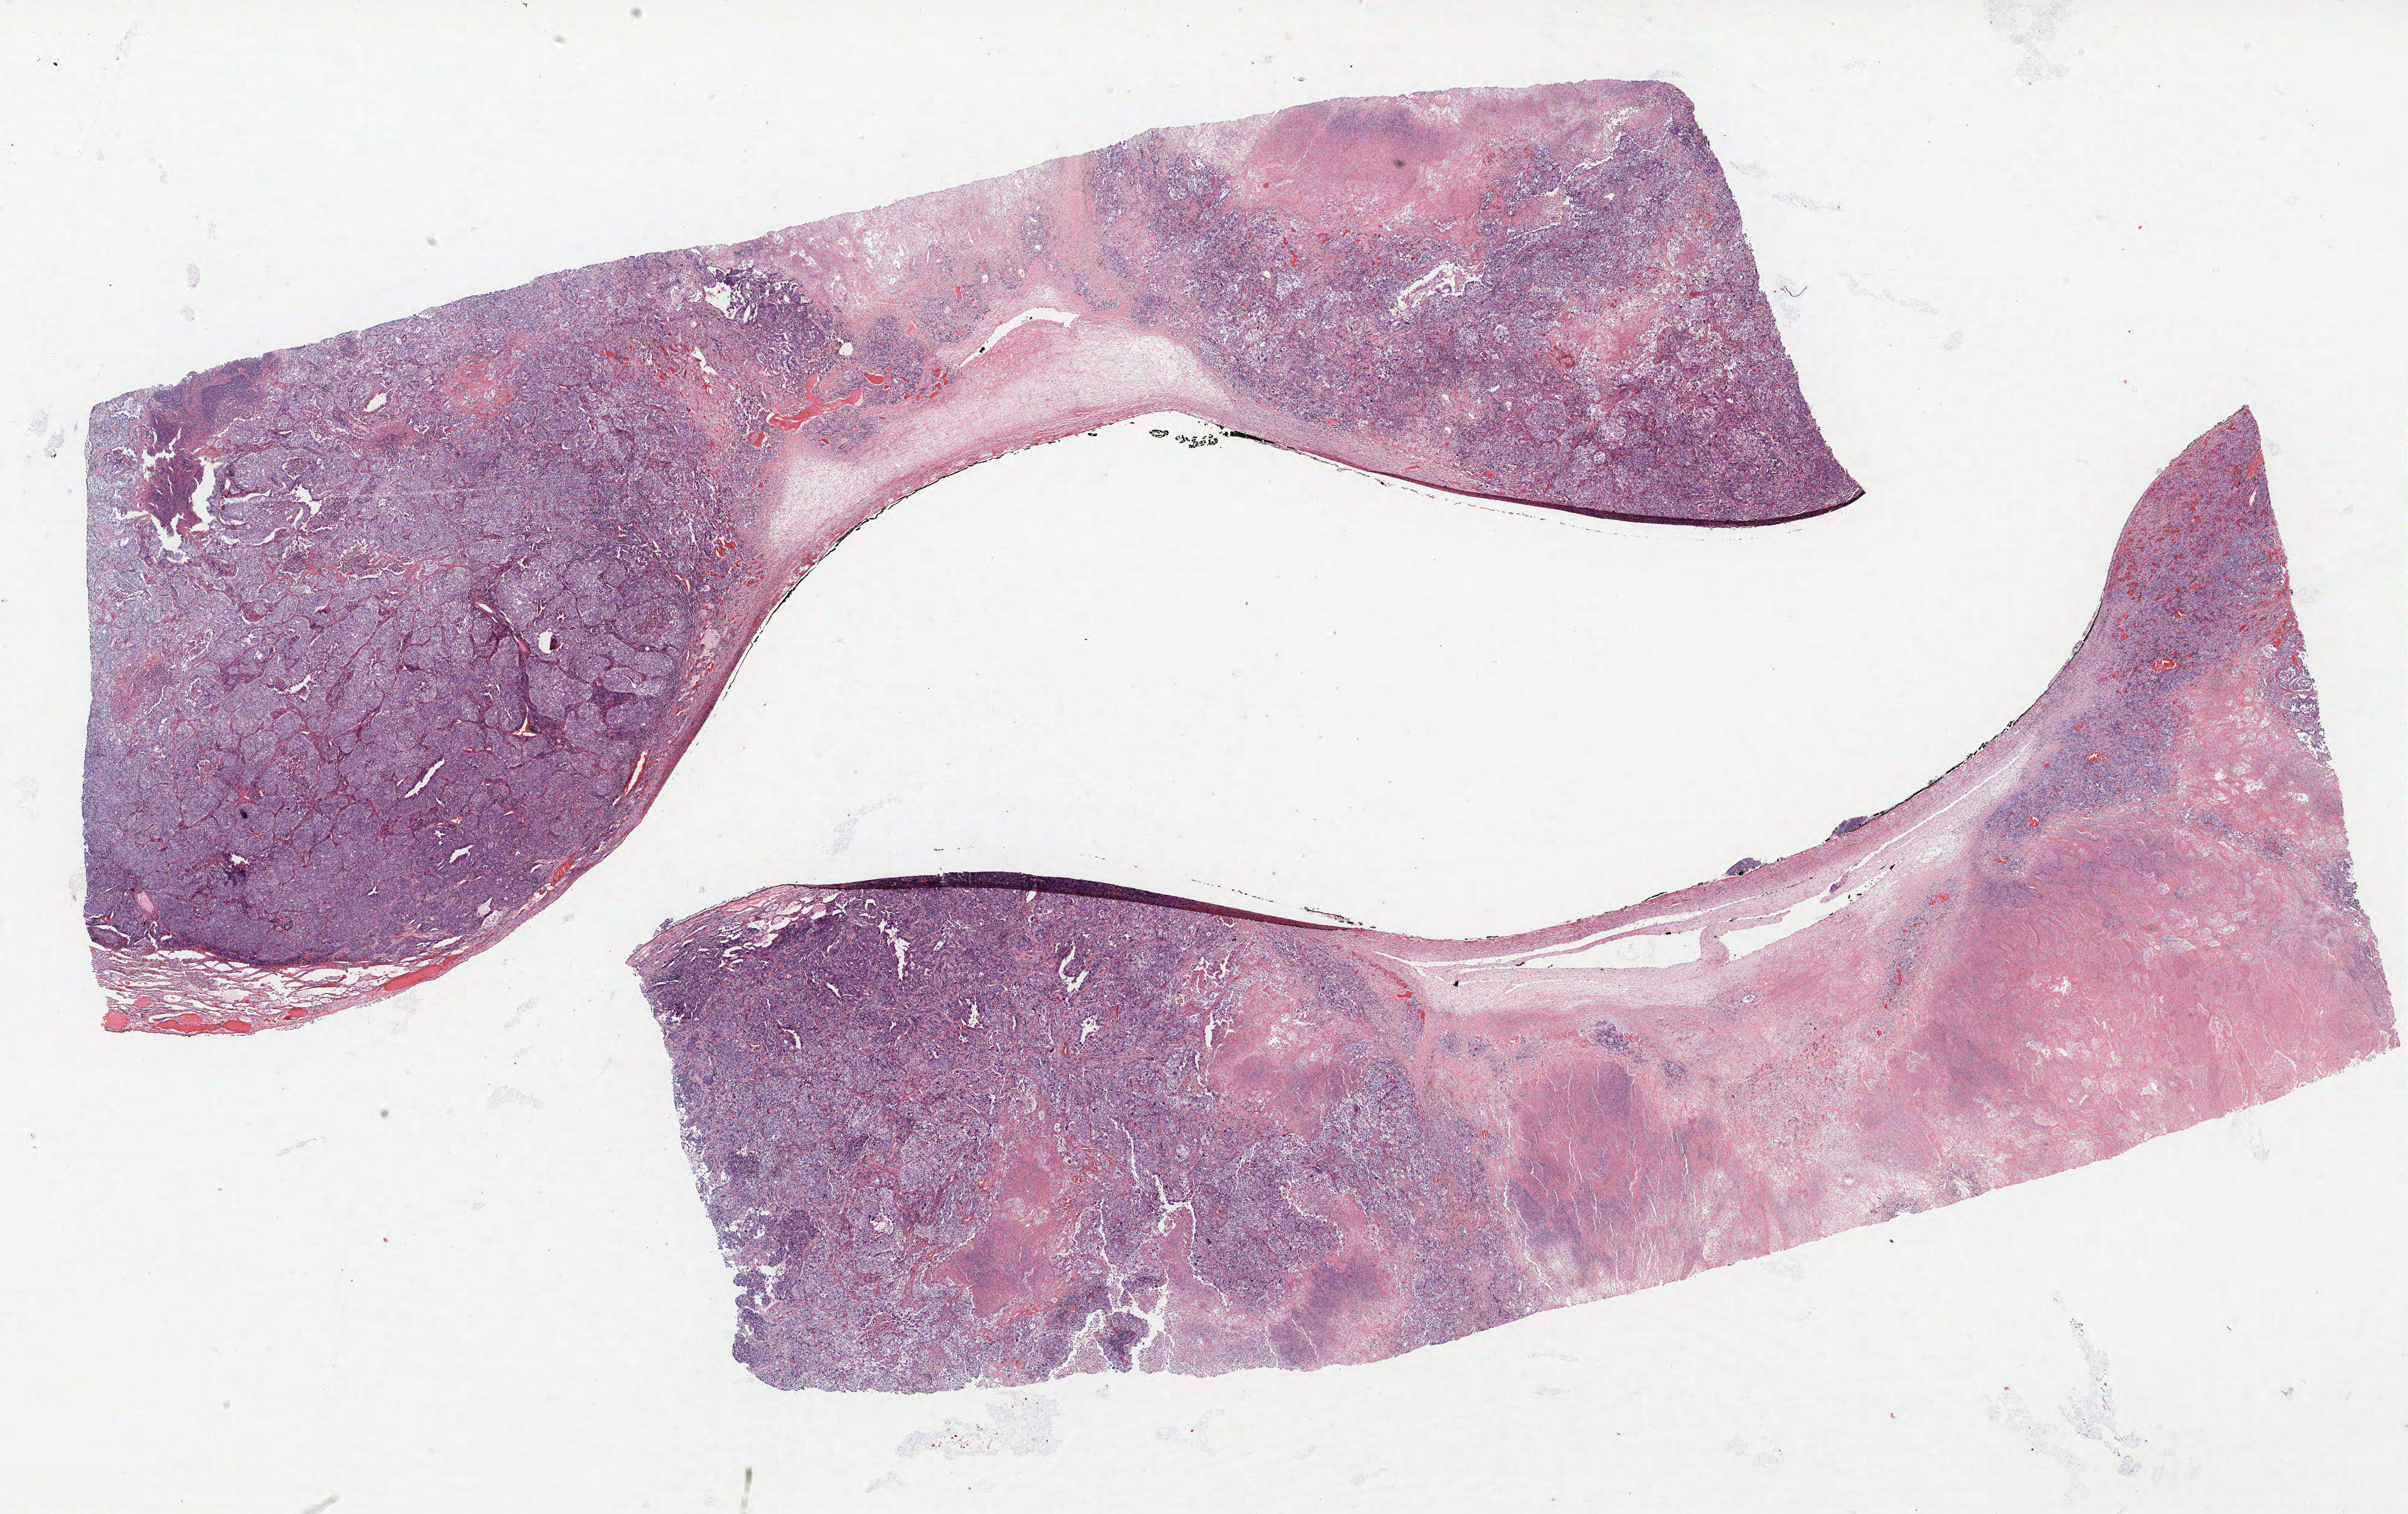
Hematoxylin and eosin (H&E) stained whole-slide image, shown as a low-resolution overview of the whole scanned area (about 31.7 x 19.9 mm), formalin-fixed paraffin-embedded (FFPE) section, lung tissue. Female patient, aged 56 at enrolment. Grade: poorly differentiated (G3).
- participant's lung-cancer diagnosis: Adenocarcinoma, NOS
- tumour size (pathology): 60 mm
- ICD-O-3 topography: lower lobe of lung (C34.3)
- primary tumour location (clinical record): right lower lobe
- stage (AJCC 6th edition): IIB